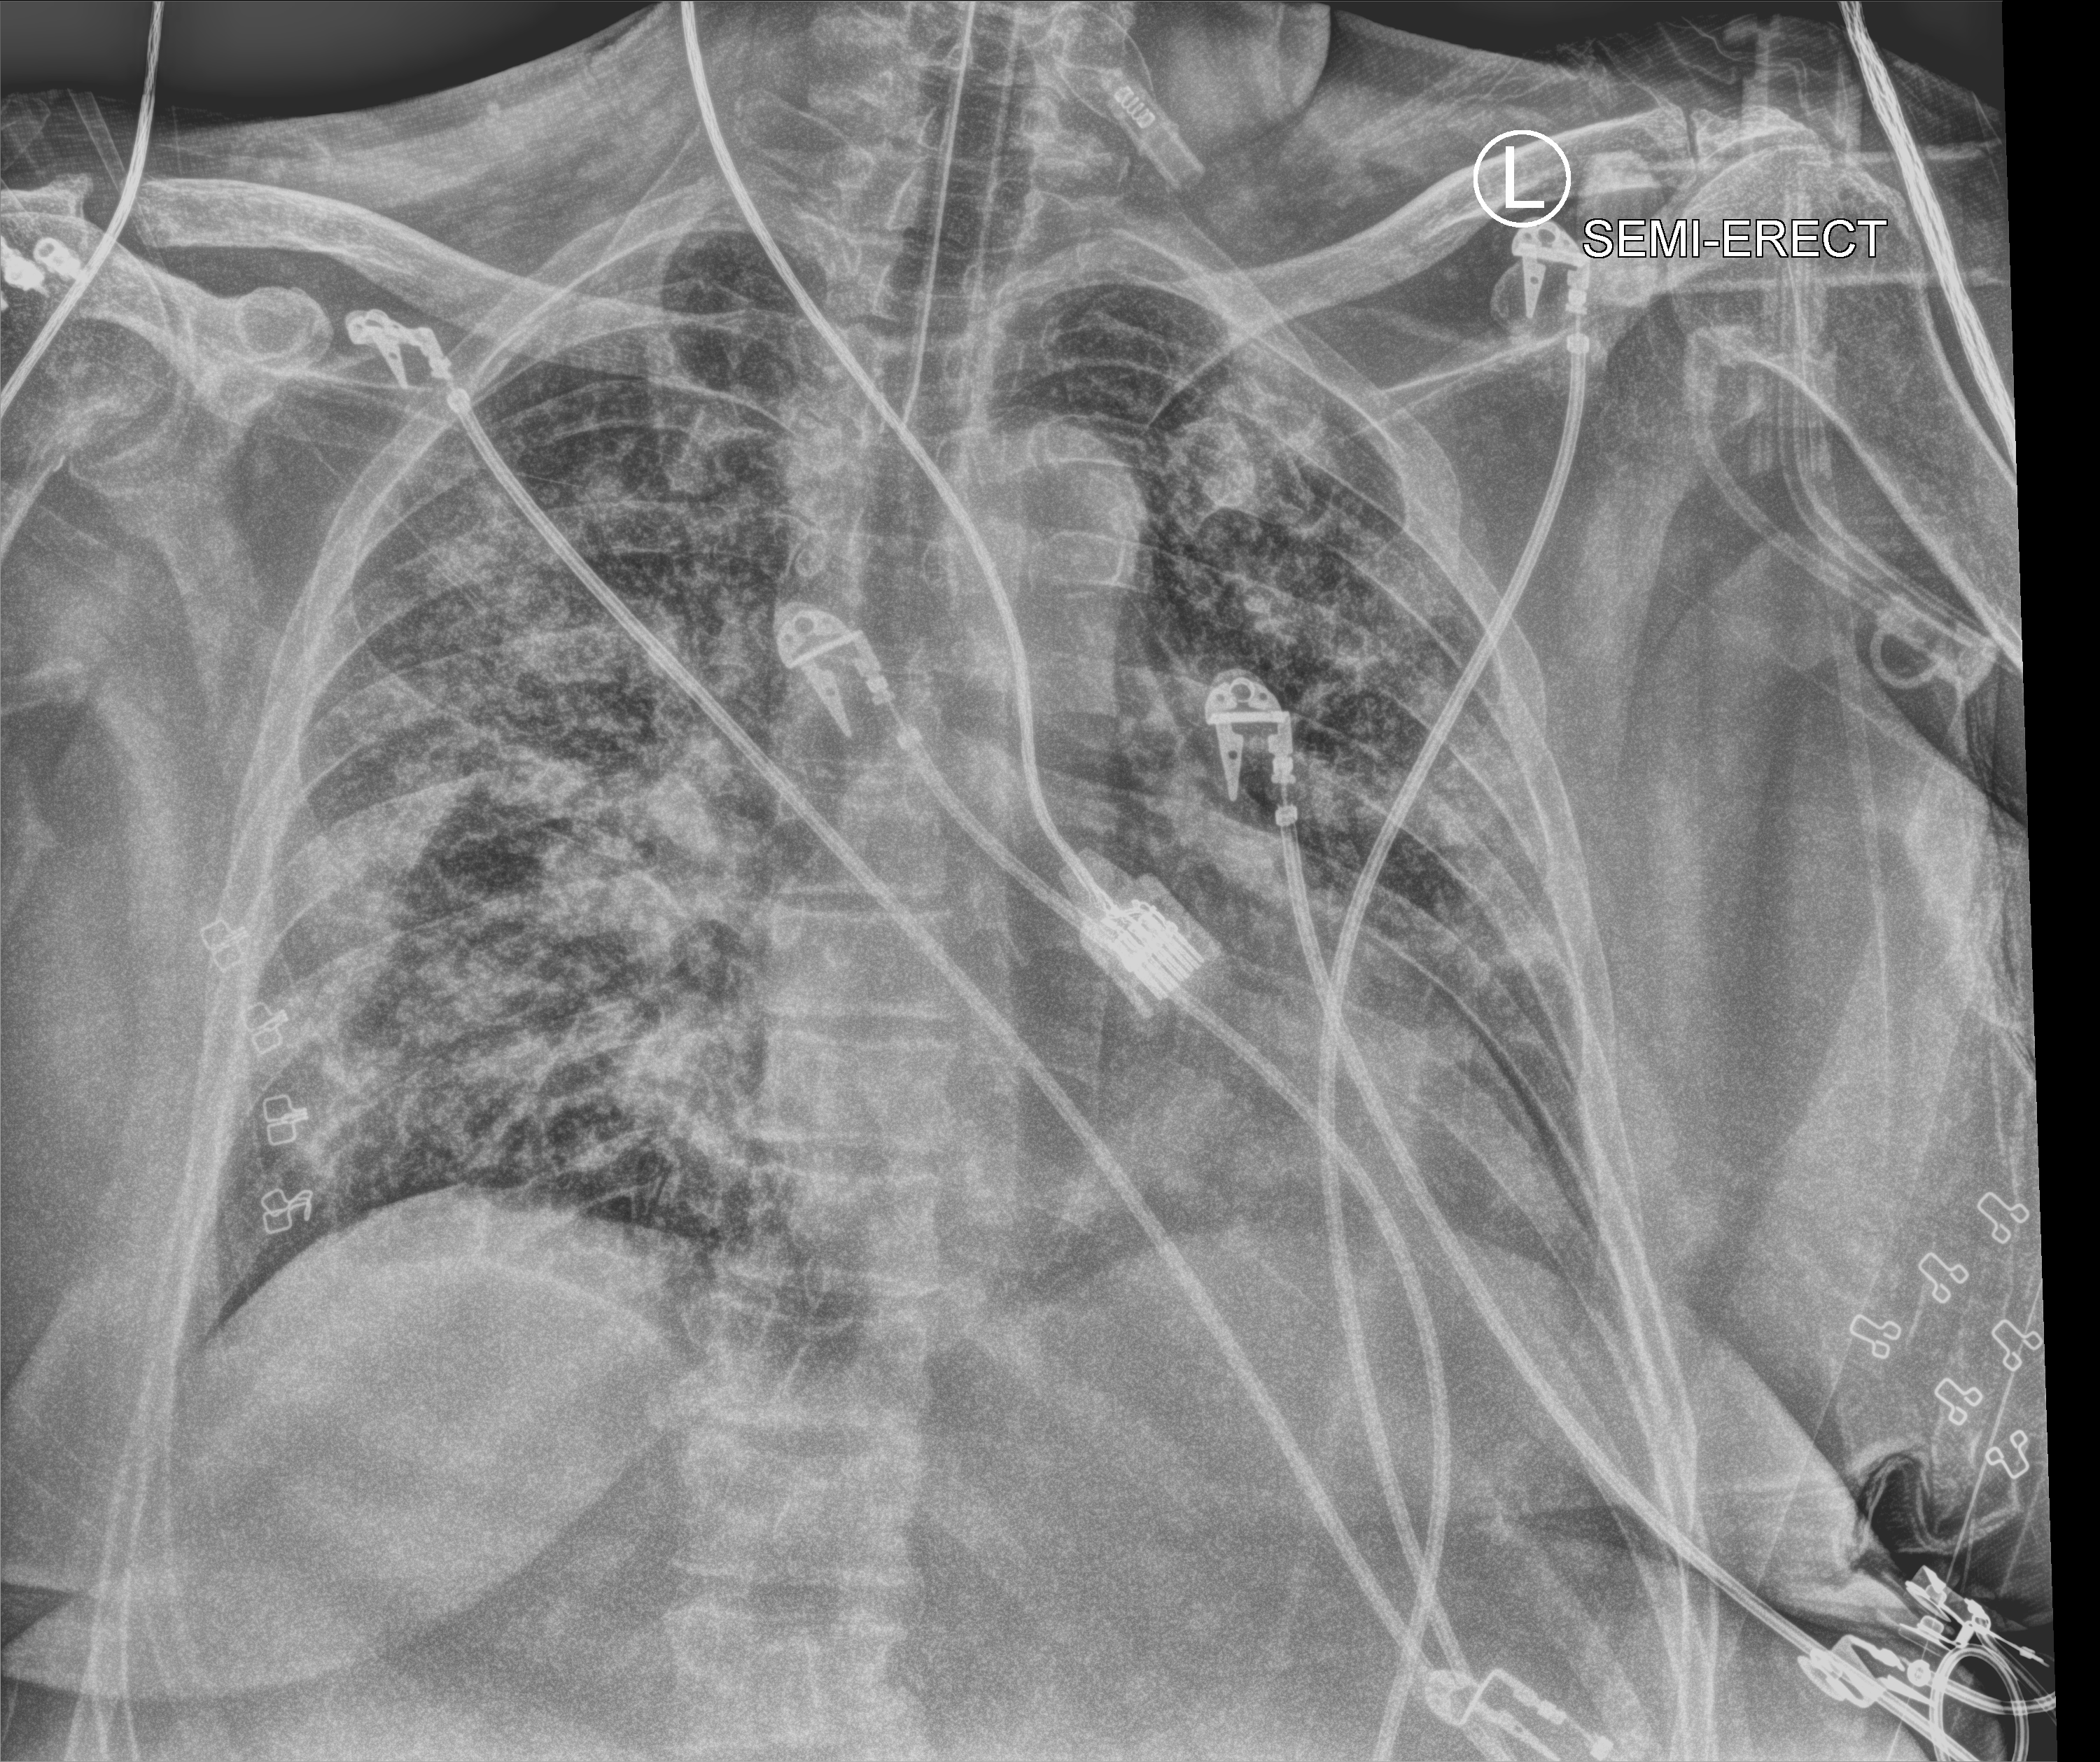
Bedside chest radiograph (computed radiography); anteroposterior (AP) projection. Female patient hospitalised with COVID-19, age 60–74 years.
From the hospital-stay record, not from the radiograph (when in the stay this image was taken is not recorded): chronic kidney disease (admission record): no; length of hospital stay: 19 days.